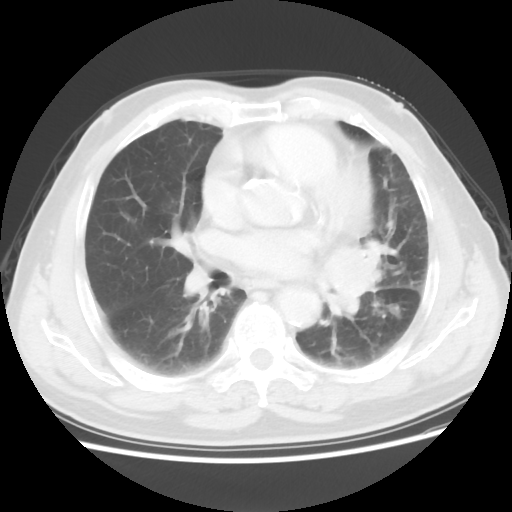
Chest CT, one axial slice. Position 30 of 56 along the scan axis. Reconstruction kernel STANDARD. 120 kVp. Lung window (W 1500 / L -600 HU). 512 × 512 image matrix, field of view 360 × 360 mm. Male patient, age 75 years. Case-level facts recorded for this patient, not image findings: clinical TNM (as recorded): T3 N0 M0.
Annotated regions visible in this slice (bounding box drawn by a radiologist):
- lung tumour (recorded histology: squamous cell carcinoma): bounding box <322,238,391,319> (left, top, right, bottom; pixels)